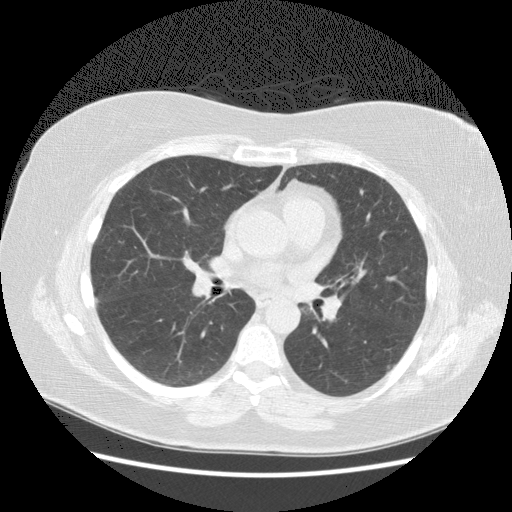
Low-dose screening chest CT, axial slice; first (baseline) screen; lung window (W 1500 / L -600 HU); standard (soft-tissue) reconstruction kernel (STANDARD); slice 85 of 154 in the series. Female, age 57 years at enrolment.
Expert reader's lesion annotation, bounding box [x1, y1, x2, y2] px = [377, 349, 407, 384]. Screening reader's record for this exam: no non-calcified nodule ≥4 mm recorded. Participant outcome: lung cancer diagnosed 928 days after this screen — squamous cell carcinoma, NOS, left lower lobe, poorly differentiated (G3), stage IB (AJCC 6th edition), 40 mm at pathology.